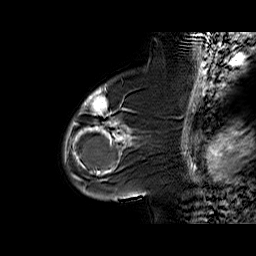
Breast MRI (dynamic contrast-enhanced), one sagittal slice. Position 43 of 60 along the scan axis. Dynamic contrast-enhanced series, time point 2 of 6 at this slice position (early post-contrast). 1.5 T. TE 6.3 ms, TR 32.4 ms. 4 mm slice thickness. 256 × 256 image matrix, field of view 200 × 200 mm. Female patient. Case-level facts recorded for this patient, not image findings: setting: breast cancer imaged before/during neoadjuvant chemotherapy; receptor status: triple-negative.
Structures marked on this image (semi-automatic segmentation, software-assisted and operator-edited):
- analysis volume of interest (the breast-tissue region the enhancement analysis was run in; not a lesion): bounding box <65,88,142,187> (left, top, right, bottom; pixels)
- tumour enhancement mask (voxels above the 100 % enhancement threshold inside the analysis volume of interest): <72,88,132,175>